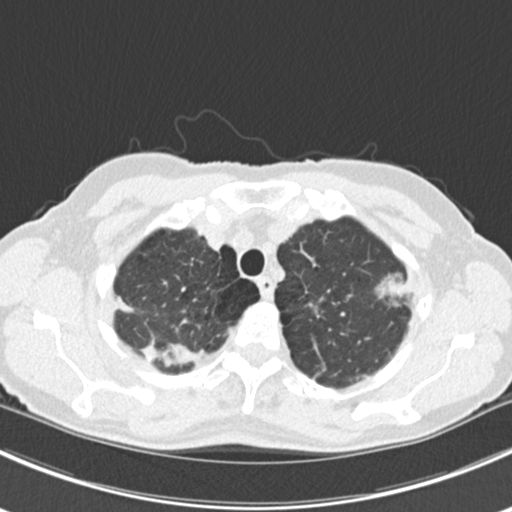
Axial slice from a low-dose chest CT screening exam; baseline annual screen; lung window (W 1500 / L -600 HU); standard (soft-tissue) reconstruction kernel (B30f). Female participant, aged 63 years at enrolment.
Expert-annotated lung lesion, bounding box <366,263,420,319> (left, top, right, bottom; pixels). The screening reader recorded 10 non-calcified nodules or masses ≥4 mm on this exam (right lower lobe, right lower lobe, left lower lobe, left lower lobe, right middle lobe, right lower lobe, left lower lobe, left upper lobe, right upper lobe, left upper lobe); which of them this box marks is not recorded. Official screen result: positive, change unspecified: nodule(s) >= 4 mm or enlarging nodule(s), mass(es), or other non-specific abnormalities suspicious for lung cancer. Lung cancer was diagnosed 751 days after this screen (after the third annual screen): bronchiolo-alveolar adenocarcinoma, NOS, right upper lobe, right middle lobe, right lower lobe, left upper lobe, left lower lobe, moderately differentiated (G2), stage IV (AJCC 6th edition).